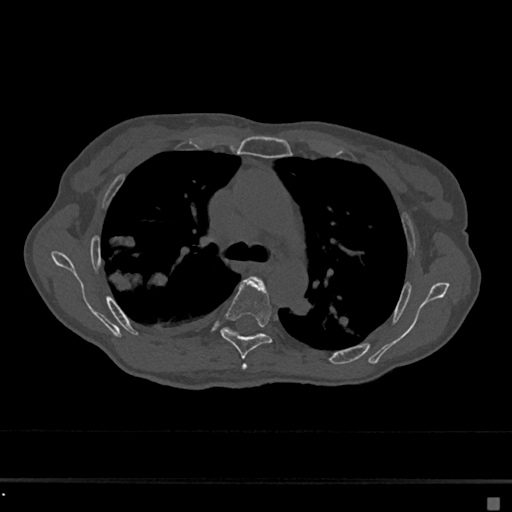
CT including the spine, one axial slice; position 460 of 797 along the scan axis; bone window (W 1800 / L 400 HU); 0.5 mm slice thickness; 512 × 512 image matrix, field of view 360 × 360 mm. Patient: female, 68 years. Case-level facts recorded for this patient, not image findings: primary cancer: renal.
Structures marked on this image (semi-automatically segmented with operator editing):
- T4 vertebra: bounding box <241,276,264,370> (left, top, right, bottom; pixels)
- T5 vertebra: <220,279,272,359>
- T6 vertebra: <227,328,235,333>